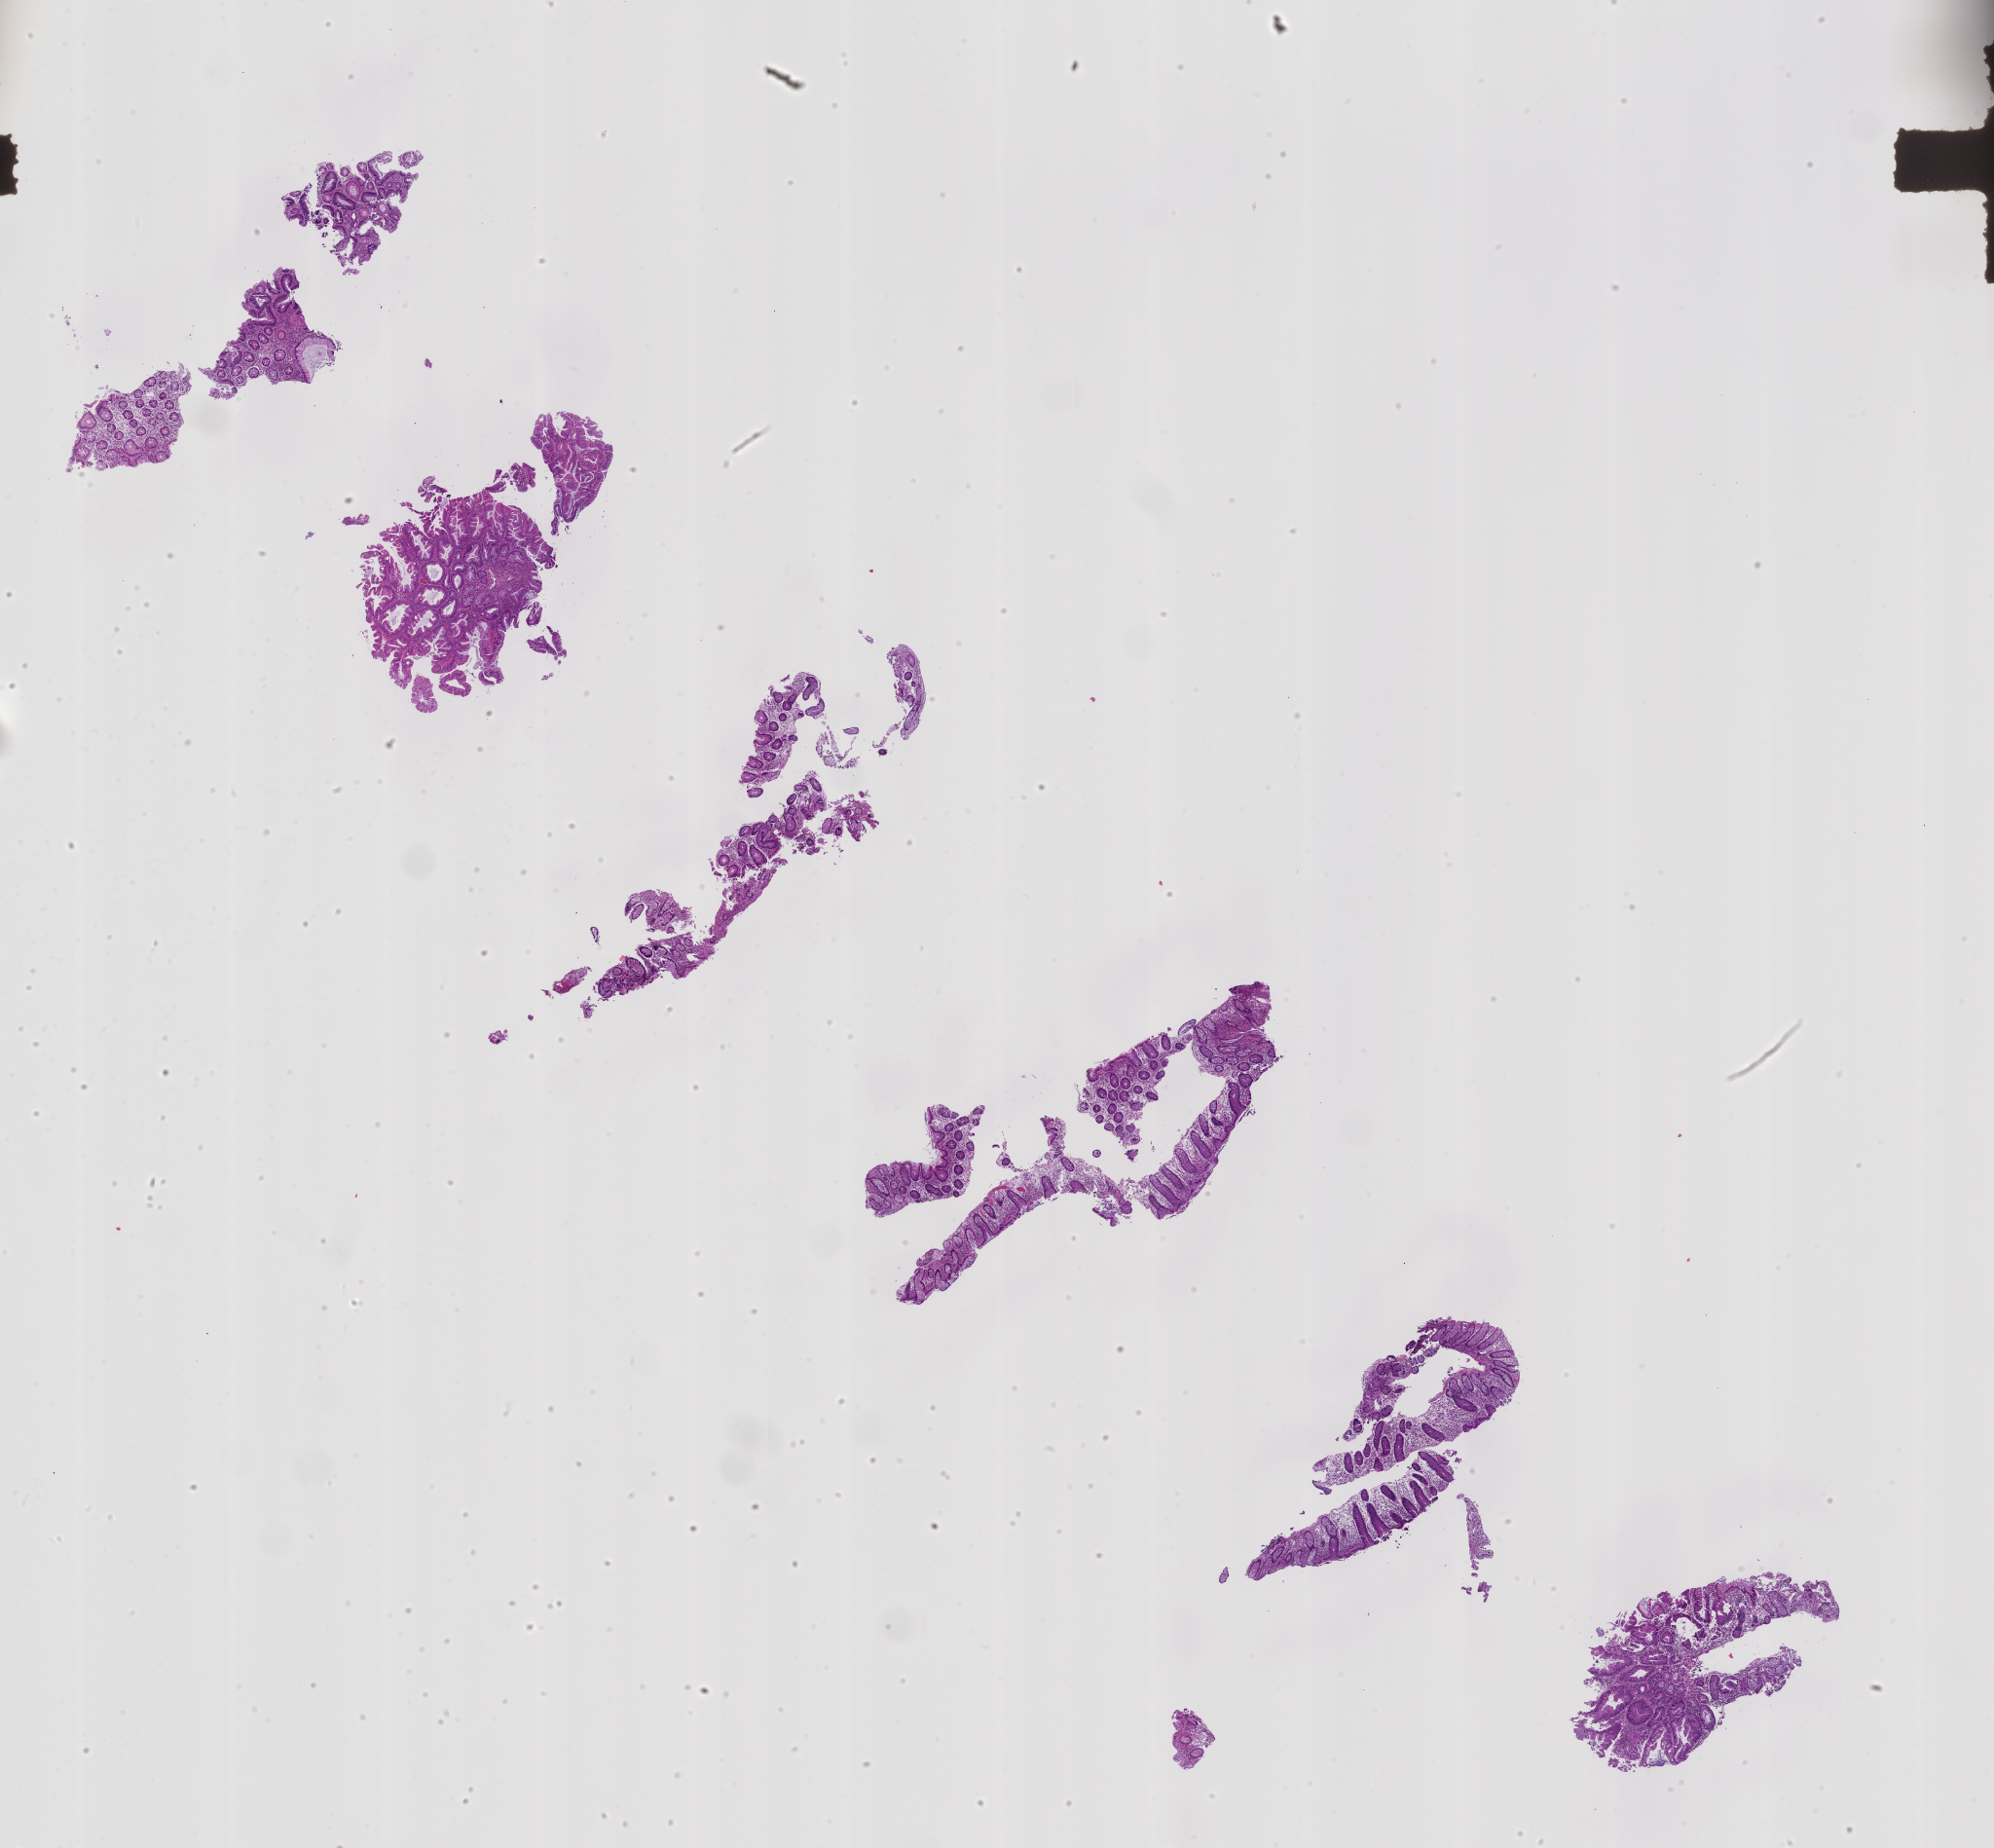
Haematoxylin and eosin whole-slide image of a colon biopsy — whole scanned area (about 16.4 x 15.2 mm) shown as a low-resolution overview, formalin-fixed, paraffin-embedded (FFPE) tissue, cecum. Female patient.
Lesion category (as recorded): premalignant.